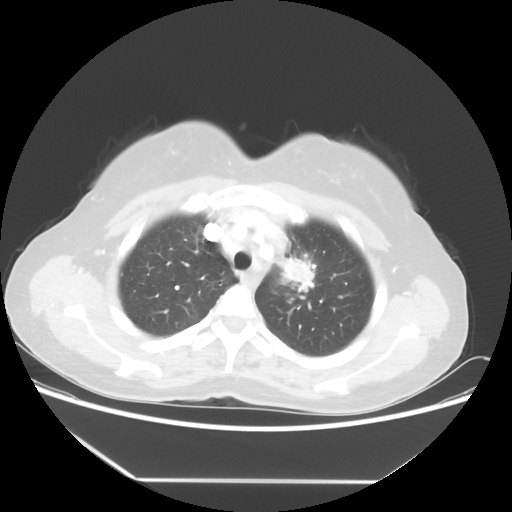
Chest CT, one axial slice; position 42 of 52 along the scan axis; reconstruction kernel STANDARD; 100 kVp; lung window (W 1500 / L -600 HU); 512 × 512 image matrix. Female patient, age 50 years. From the clinical record (not read from this slice): clinical TNM (as recorded): T2 N3 M0.
Annotated regions visible in this slice (rectangle marked by the reading radiologist):
- lung tumour (recorded histology: adenocarcinoma): box from (x=272, y=248) to (x=314, y=293) px